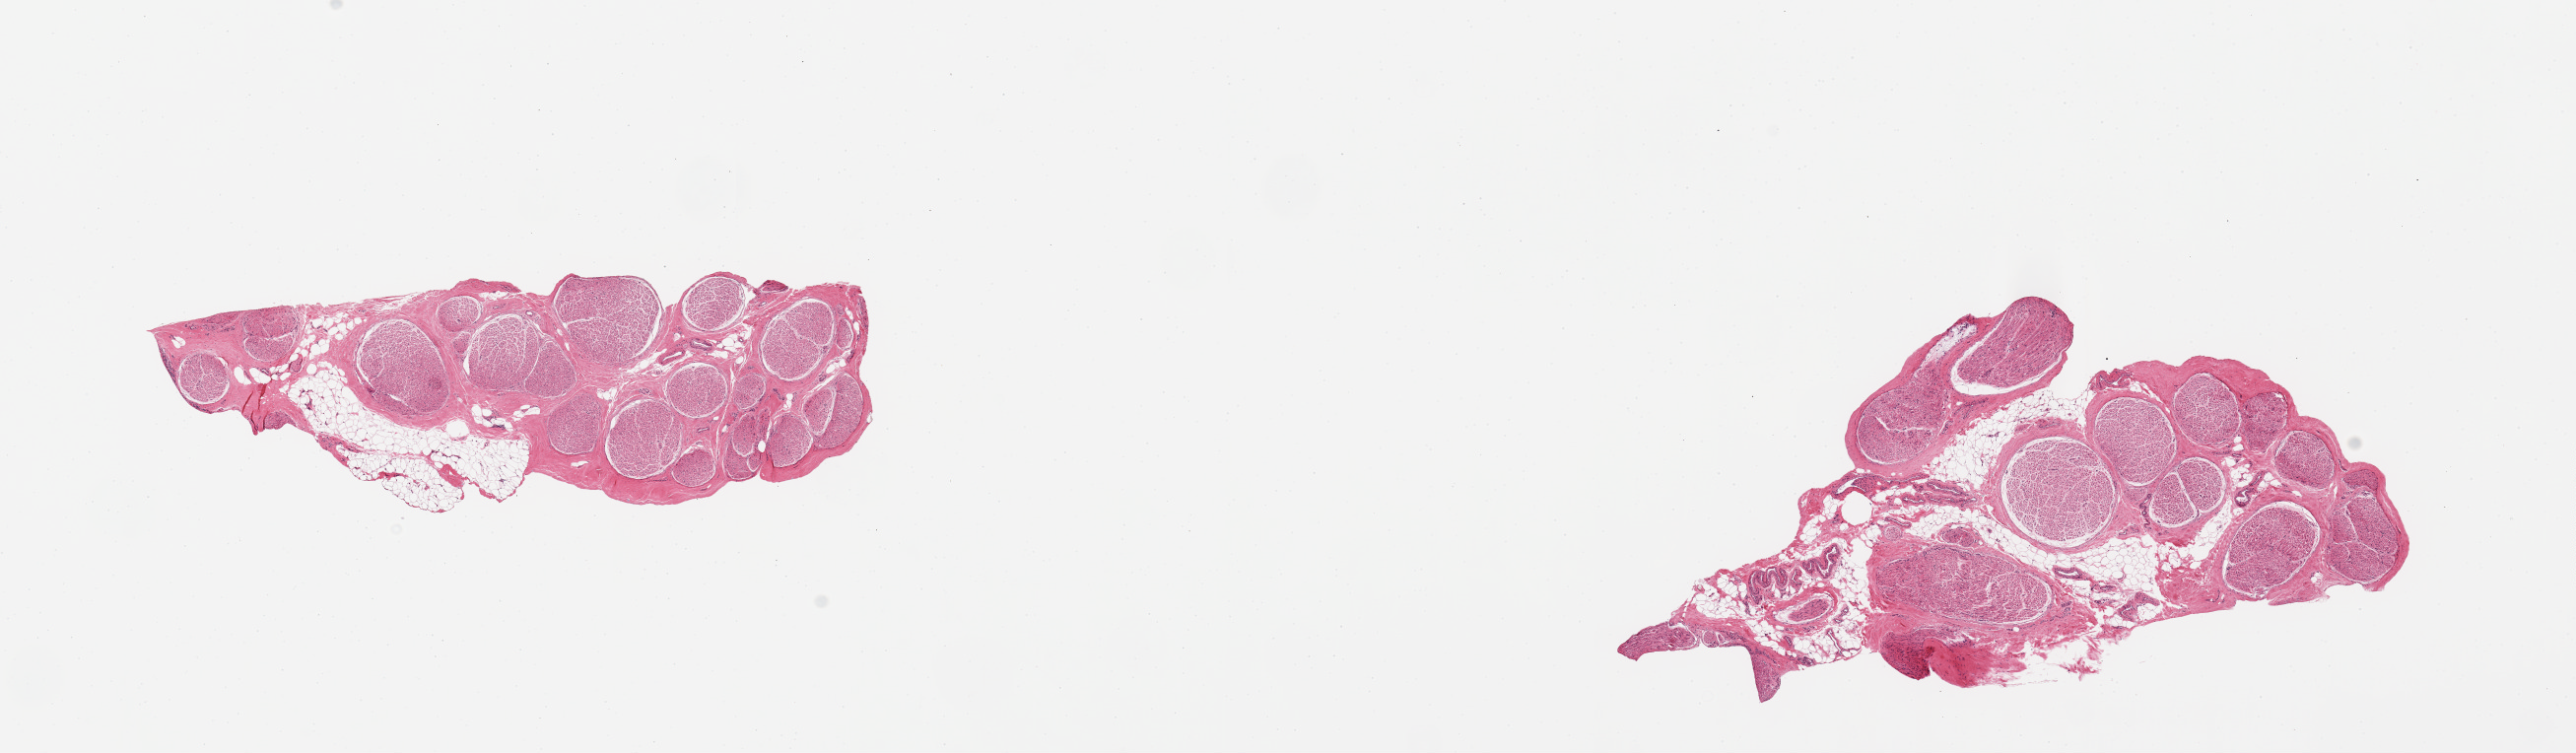
Whole-slide image, hematoxylin and eosin (H&E) stain, brightfield — low-resolution overview of the scanned area, about 20.7 x 6.0 mm (slide scanned at 20x). PAXgene-fixed, paraffin-embedded tissue. Target tissue: tibial nerve. Tissue donor sample. Donor: male.
Pathologist's review note for this sample: 2 pieces; 10% & 20% internal fat content.